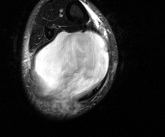
MRI of an extremity soft-tissue mass, one axial slice. Slice 44 of 81 in the series (ordered by position). T2-weighted fat-saturated. MR volume resampled by the dataset authors to the PET/CT grid (not the native acquisition matrix). 3.27 mm slice thickness. 165 × 137 image matrix. Male patient. Case-level facts recorded for this patient, not image findings: histological type: liposarcoma - round cell; grade: high; site of the primary tumour: right calf.
Structures marked on this image (expert contour drawn on MRI and transferred to this co-registered scan by the dataset authors):
- gross tumour volume (mass): bounding box <34,30,109,110> (left, top, right, bottom; pixels)